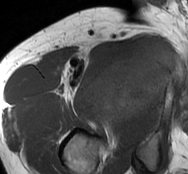
MRI of an extremity soft-tissue mass, one axial slice. Position 65 of 93 along the scan axis. MR volume resampled by the dataset authors to the PET/CT grid (not the native acquisition matrix). 3.27 mm slice thickness. 188 × 174 image matrix, field of view 184 × 170 mm. Male patient. From the clinical record (not read from this slice): histological type: undifferentiated - pleiomorphic; grade: high; site of the primary tumour: right thigh.
Annotated regions visible in this slice (expert contour drawn on MRI and transferred to this co-registered scan by the dataset authors):
- gross tumour volume including surrounding oedema: bounding box (x1, y1, x2, y2) in pixels: (93, 40, 178, 127)
- gross tumour volume (mass): (91, 42, 176, 127)